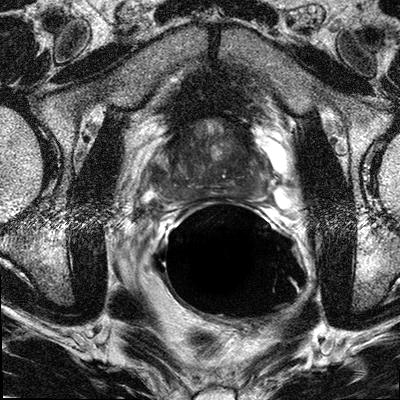
Multiparametric prostate MRI examination; 3 images, each a single mid-volume slice chosen by position (not for content). Treatment context recorded for this patient: Surgery.
Image 1: T2-weighted axial slice, series "T2W_TSE_AX", slice 17 of 32, 3 mm slice thickness.
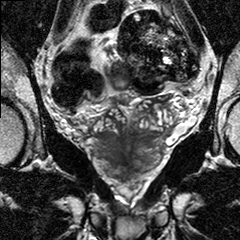
Image 2: coronal T2-weighted image, slice 13 of 24.
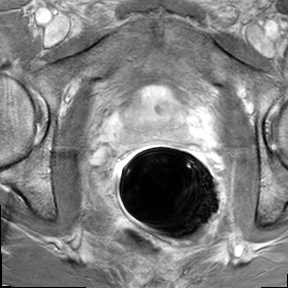
Image 3: DCE (dynamic gadolinium-enhanced) axial slice, series "AX BLISS_GAD_8", slice 17 of 32, dynamic phase 5 of 8, 6 mm slice thickness.
Radiologist's MRI report for this examination:
FINDINGS: The prostate gland measures 5.0 (TV) x 3.3 (AP) x 3.5 (CC) cm and the prostate volume measures 30.0 cc. The zonal anatomy of the prostate gland is preserved. There is diffuse low T2 signal in left and right posterolateral peripheral zones (PZ) with a dominate nodule in the right posterolateral peripheral zone measuring 2.0 x 0.8 cm in the mid third of the gland and dominant nodule in the left posterolateral PZ measuring 1.2 x 1.0 cm. The posterolateral nodules extend to the prostatic capsule without definitive extracapsular extension. An additional nodule is visualized and the anterior aspect of the left peripheral zone at the 2:00 position which bulges the capsule with no definite extracapsular involvement. Within these areas, suspicious contrast enhancement is visualized with a rapid wash-in and washout pattern. No neurovascular involvement is visualized. The seminal vesicles are not involved. The urinary bladder and rectum are uninvolved. A prominent venous plexus is visualized. There is benign prostatic hypertrophy. The diagnostic value of the lymph node sequences is reduced secondary to extensive air and stool throughout the large bowel. A right obturator lymph node is visualized measuring 0.8 x 0.5 cm (slice location 50, series 701). No suspicious bone marrow signal abnormalities are seen. Multiplanar reconstructions, subtraction images, and CAD analysis of the dynamic series for assessment of the kinetic information facilitated the interpretation of the exam.
IMPRESSION:
1. Bilateral prostate cancer, left greater than right, with no manifest extracapsular extension; capsular infiltration, especially left posterior lateral towards the left neurovascular bundle, is possible. No MRI evidence of neurovascular bundle or seminal vesicle involvement. 2. Limited evaluation for pelvic lymphadenopathy secondary to the bowel and stool-filled colon. Indeterminate 8 mm right obturator lymph node (superior lateral to the right seminal vesicles); recommend CT of the pelvis for further evaluation. 3. Benign prostatic hypertrophy.

Prostate biopsy pathology (as recorded):
The specimen is received fixed in a single container labeled with the patient's name, hospital number and Prostate. The specimen consists of multiple core fragments of tan soft tissue measuring from 1.5cm to 2cm in length and 0.1cm in diameter. The specimen is submitted in six cassettes as follows: 1-right PZ, 2-right PZ TZ, 3-right apex, 4-left PZ, 5-left PZ TZ, 6-left apex.- Specimen(s) Received PROSTATE BIOPSIES: 1. RIGHT PZ: PROSTATIC ADENOCARCINOMA, GLEASON SCORE 3+3=6/10, INVOLVING 40% OF THE TISSUE EXAMINED (TWO CORES). 2. RIGHT PZ/TZ: BENIGN PROSTATIC TISSUE, NO TUMOR IDENTIFIED. 3. RIGHT APEX: PROSTATIC ADENOCARCINOMA, GLEASON SCORE 3+3=6/10, INVOLVING 30% OF THE TISSUE EXAMINED (TWO CORES). 4. LEFT PZ: PROSTATIC ADENOCARCINOMA, GLEASON SCORE 3+3=6/10, INVOLVING 40% OF THE TISSUE EXAMINED (TWO CORES). 5. LEFT PZ/TZ: PROSTATIC ADENOCARCINOMA, GLEASON SCORE 3+3=6/10, INVOLVING 5% OF THE TISSUE EXAMINED (ONE CORE). 6. LEFT APEX: PROSTATIC ADENOCARCINOMA, GLEASON SCORE 3+3=6/10, INVOLVING 40% OF THE TISSUE EXAMINED (TWO CORES). NOTE: PERINEURAL INVASION PRESENT.

Prostatectomy specimen pathology (as recorded; the surgery followed this MRI):
Specimen(s) Received A. "Left Pelvic Lymph Node", B. "Right Pelvic Lymph Node", C. "Bladder Neck Tissue" and D. "Prostate and Seminal Vesicles". Specimen A consists of a 4.5x1x05. cm piece of fibrofatty tissue from which a 4 cm whole lymph node dissected. The lymph node is serially sectioned and the entire specimen is submitted in two cassettes labeled A1 and A2. Specimen B consists of a 3.5x2x0.5 cm piece of fibroadipose tissue which contains a 3 cm single lymph ode. The lymph node is serially sectioned and submitted entirely in two cassettes labeled B1 and B2. Specimen C consists of a 1x0.5x0.3 cm piece of tan/white tissue. The specimen is submitted entirely in a single cassette labeled C. Specimen D consists of a 49.1 gram, 4x3x2.5 cm radical prostatectomy specimen. The attached right and left vas average 4 cm in length by 3 cm in diameter, the right and left seminal vesicles average 3.5x1.5x0.5 cm. The specimen is inked as follows: right side black and left side blue. The proximal and distal margins are taken enface and radial sectioned. The remaining specimen is transversely sectioned to reveal a vaguely nodular cut surface. Representative sections are submitted in cassettes as follows: D1 and D2 radial section, proximal bladder base margin, D3 and D4 radial section, distal urethral margin, D5 right vas and right seminal vesicle, D6 left vas and left seminal vesicle, D7 thru D10 right anterior lobe, inferior to superior, D11 thru D14 right posterior lobe, inferior to superior, D15 thru D18 left posterior lobe, inferior to superior, D19 thru D22 left anterior lobe, superior to inferior. Final Diagnosis A. LEFT PELVIC LYMPH NODE: TWO (2) REACTIVE LYMPH NODES, NO TUMOR IDENTIFIED. B. RIGHT PELVIC LYMPH NODE: FOUR (4) REACTIVE LYMPH NODES, NO TUMOR IDENTIFIED. C. BLADDER NECK TISSUE: FRAGMENT OF FIBROCOLLAGENOUS TISSUE, NO TUMOR IDENTIFIED. D. PROSTATE AND SEMINAL VESICLES: Prostate Size: Weight: 49.1g Size: 4x3x2.5cm Lymph Node Sampling: Pelvic lymph node dissection Histologic Type: Adenocarcinoma Histologic Grade: Primary Pattern Grade 3 Secondary Pattern Grade 4 Total Gleason Score: 3+4=7/10 Tumor Quantitation: Proportion (percentage) of prostate involved by tumor: 50% Extraprostatic Extension: Not identified. Seminal Vesicle Invasion: Not identified Margins: Margins uninvolved by invasive carcinoma Lymph-Vascular Invasion: Not identified Perineural Invasion: Present
Pathologic Staging (pTNM) Primary Tumor (pT) pT2c: Bilateral disease Regional Lymph Nodes (pN) pNo: No regional lymph node metastasis Specify: Number examined: 7 Number involved: 0
Distant Metastasis (pM) pMx: Not applicable AJCC Pathologic Stage (7th edition): (pT2c, pNo)
Clinical diagnosis and History: Prostate cancer